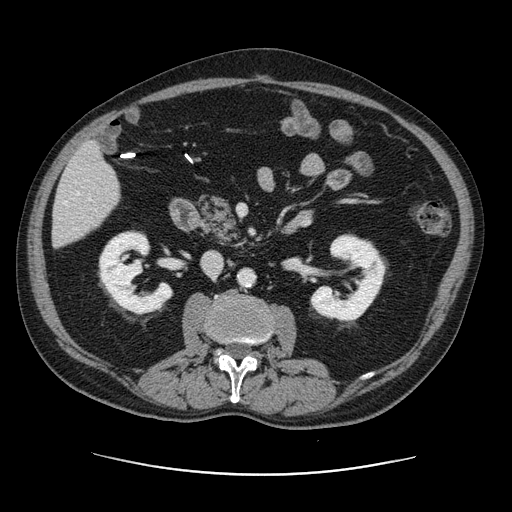
Contrast-enhanced abdominal CT, one axial slice; position 43 of 141 along the scan axis; 120 kVp; intravenous contrast given; soft-tissue window (W 400 / L 40 HU); 2.5 mm slice thickness; 512 × 512 image matrix, field of view 395 × 395 mm. Male patient, age 72 years. From the clinical record (not read from this slice): diagnosis: colorectal cancer liver metastases, imaged before liver resection; multiple liver metastases: yes; largest metastasis: 5.4 cm; disease in both lobes: yes.
Outlined on this slice (expert manual segmentation):
- hepatic veins: bounding box <64,192,91,204> (left, top, right, bottom; pixels)
- liver: <53,144,120,247>
- planned liver remnant (the part of the liver to remain after resection): <53,152,120,247>
- portal vein (with intrahepatic branches): <73,228,77,230>